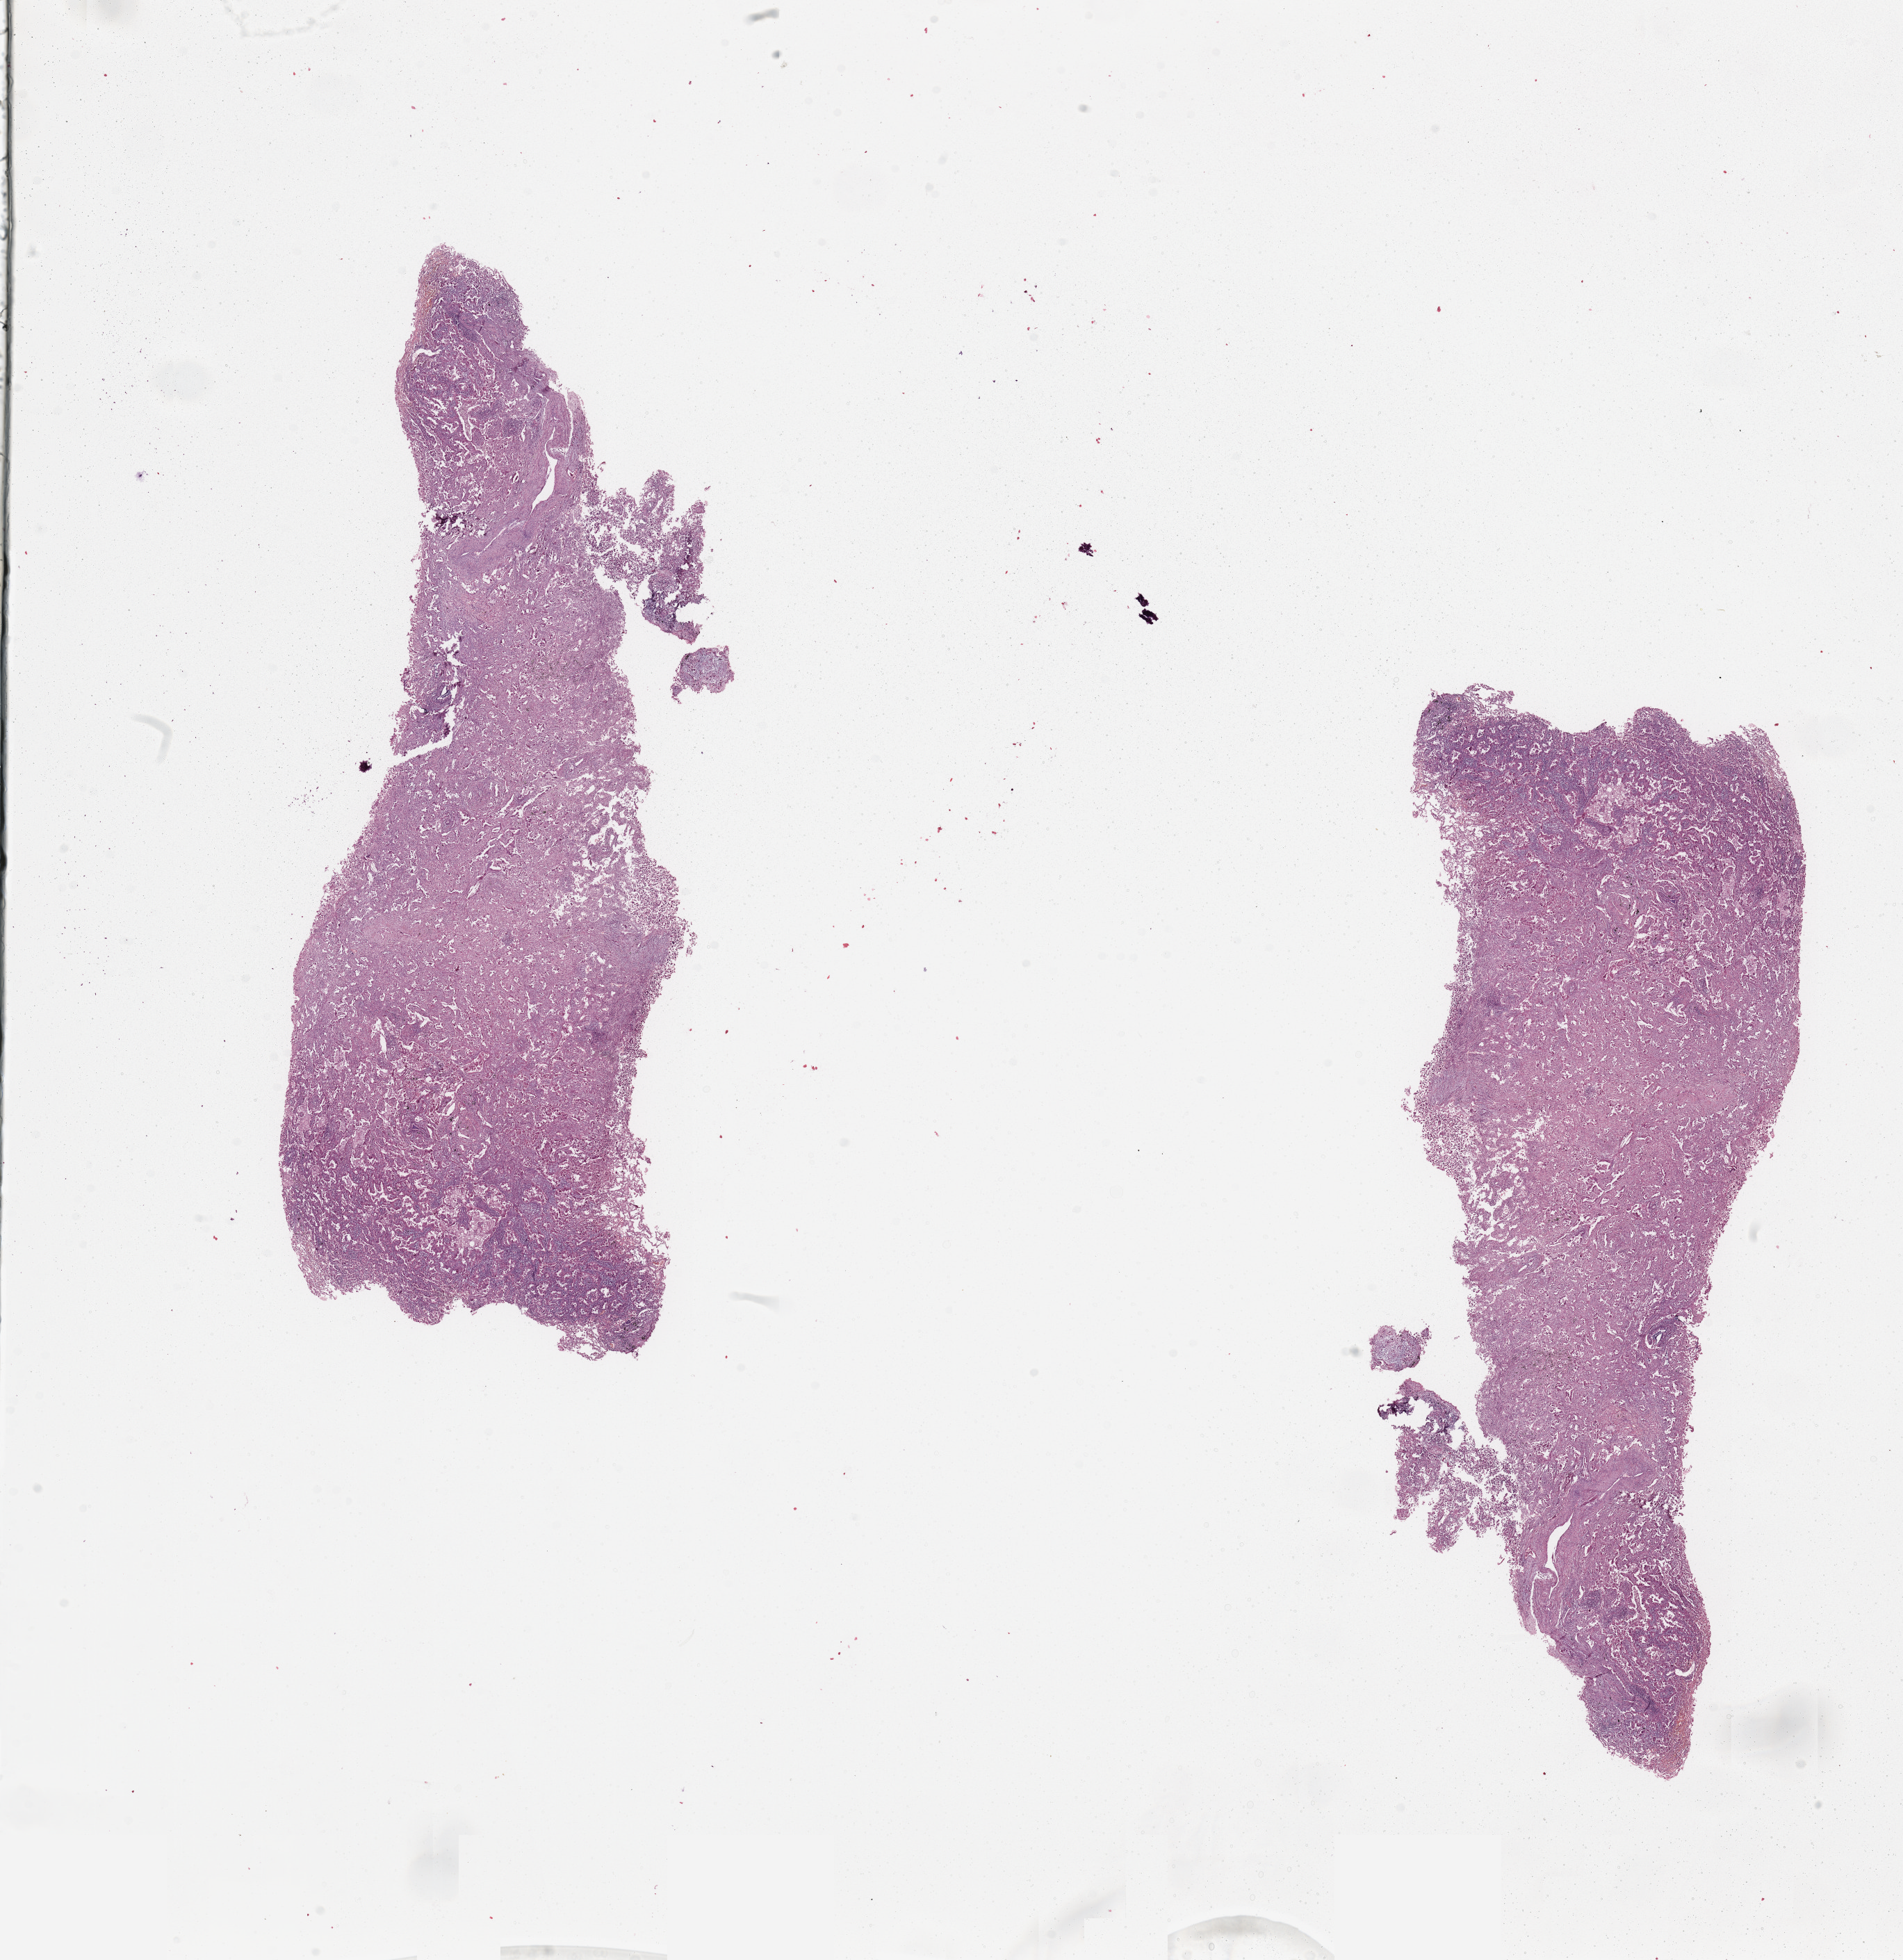
Digitized Hematoxylin and eosin (H&E) stained tissue section (whole slide), low-resolution overview of the scanned area, about 21.7 x 22.3 mm (from a 20x scan); tumour tissue sample, sampled site: lung. 63-year-old female patient. Histologic grade: G2 (moderately differentiated). Composition of this section per pathologist review: tumour nuclei 65%, necrosis 5%.
Primary tumour site (as recorded): right upper lobe. AJCC pathologic stage: IB. Histologic diagnosis: Adenocarcinoma, NOS.